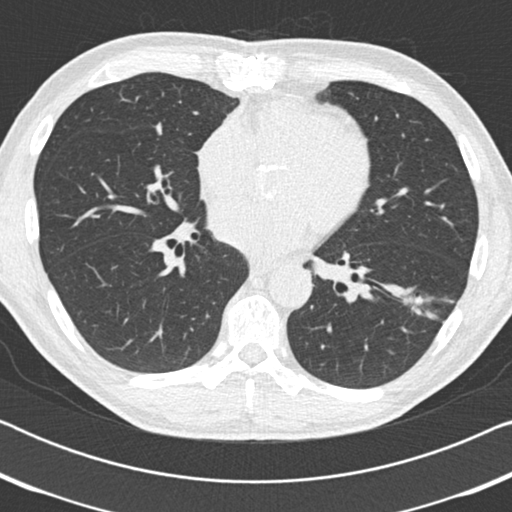
Low-dose screening chest CT, one axial slice. Position 83 of 186 along the scan axis. Reconstruction kernel B30f. 120 kVp. Lung window (W 1500 / L -600 HU). 2 mm slice thickness. 512 × 512 image matrix, field of view 330 × 330 mm.
Outlined on this slice (manually delineated by an expert):
- lesion 1 (tumor, lower lobe of left lung): bounding box [x1, y1, x2, y2] px = [404, 296, 428, 314]